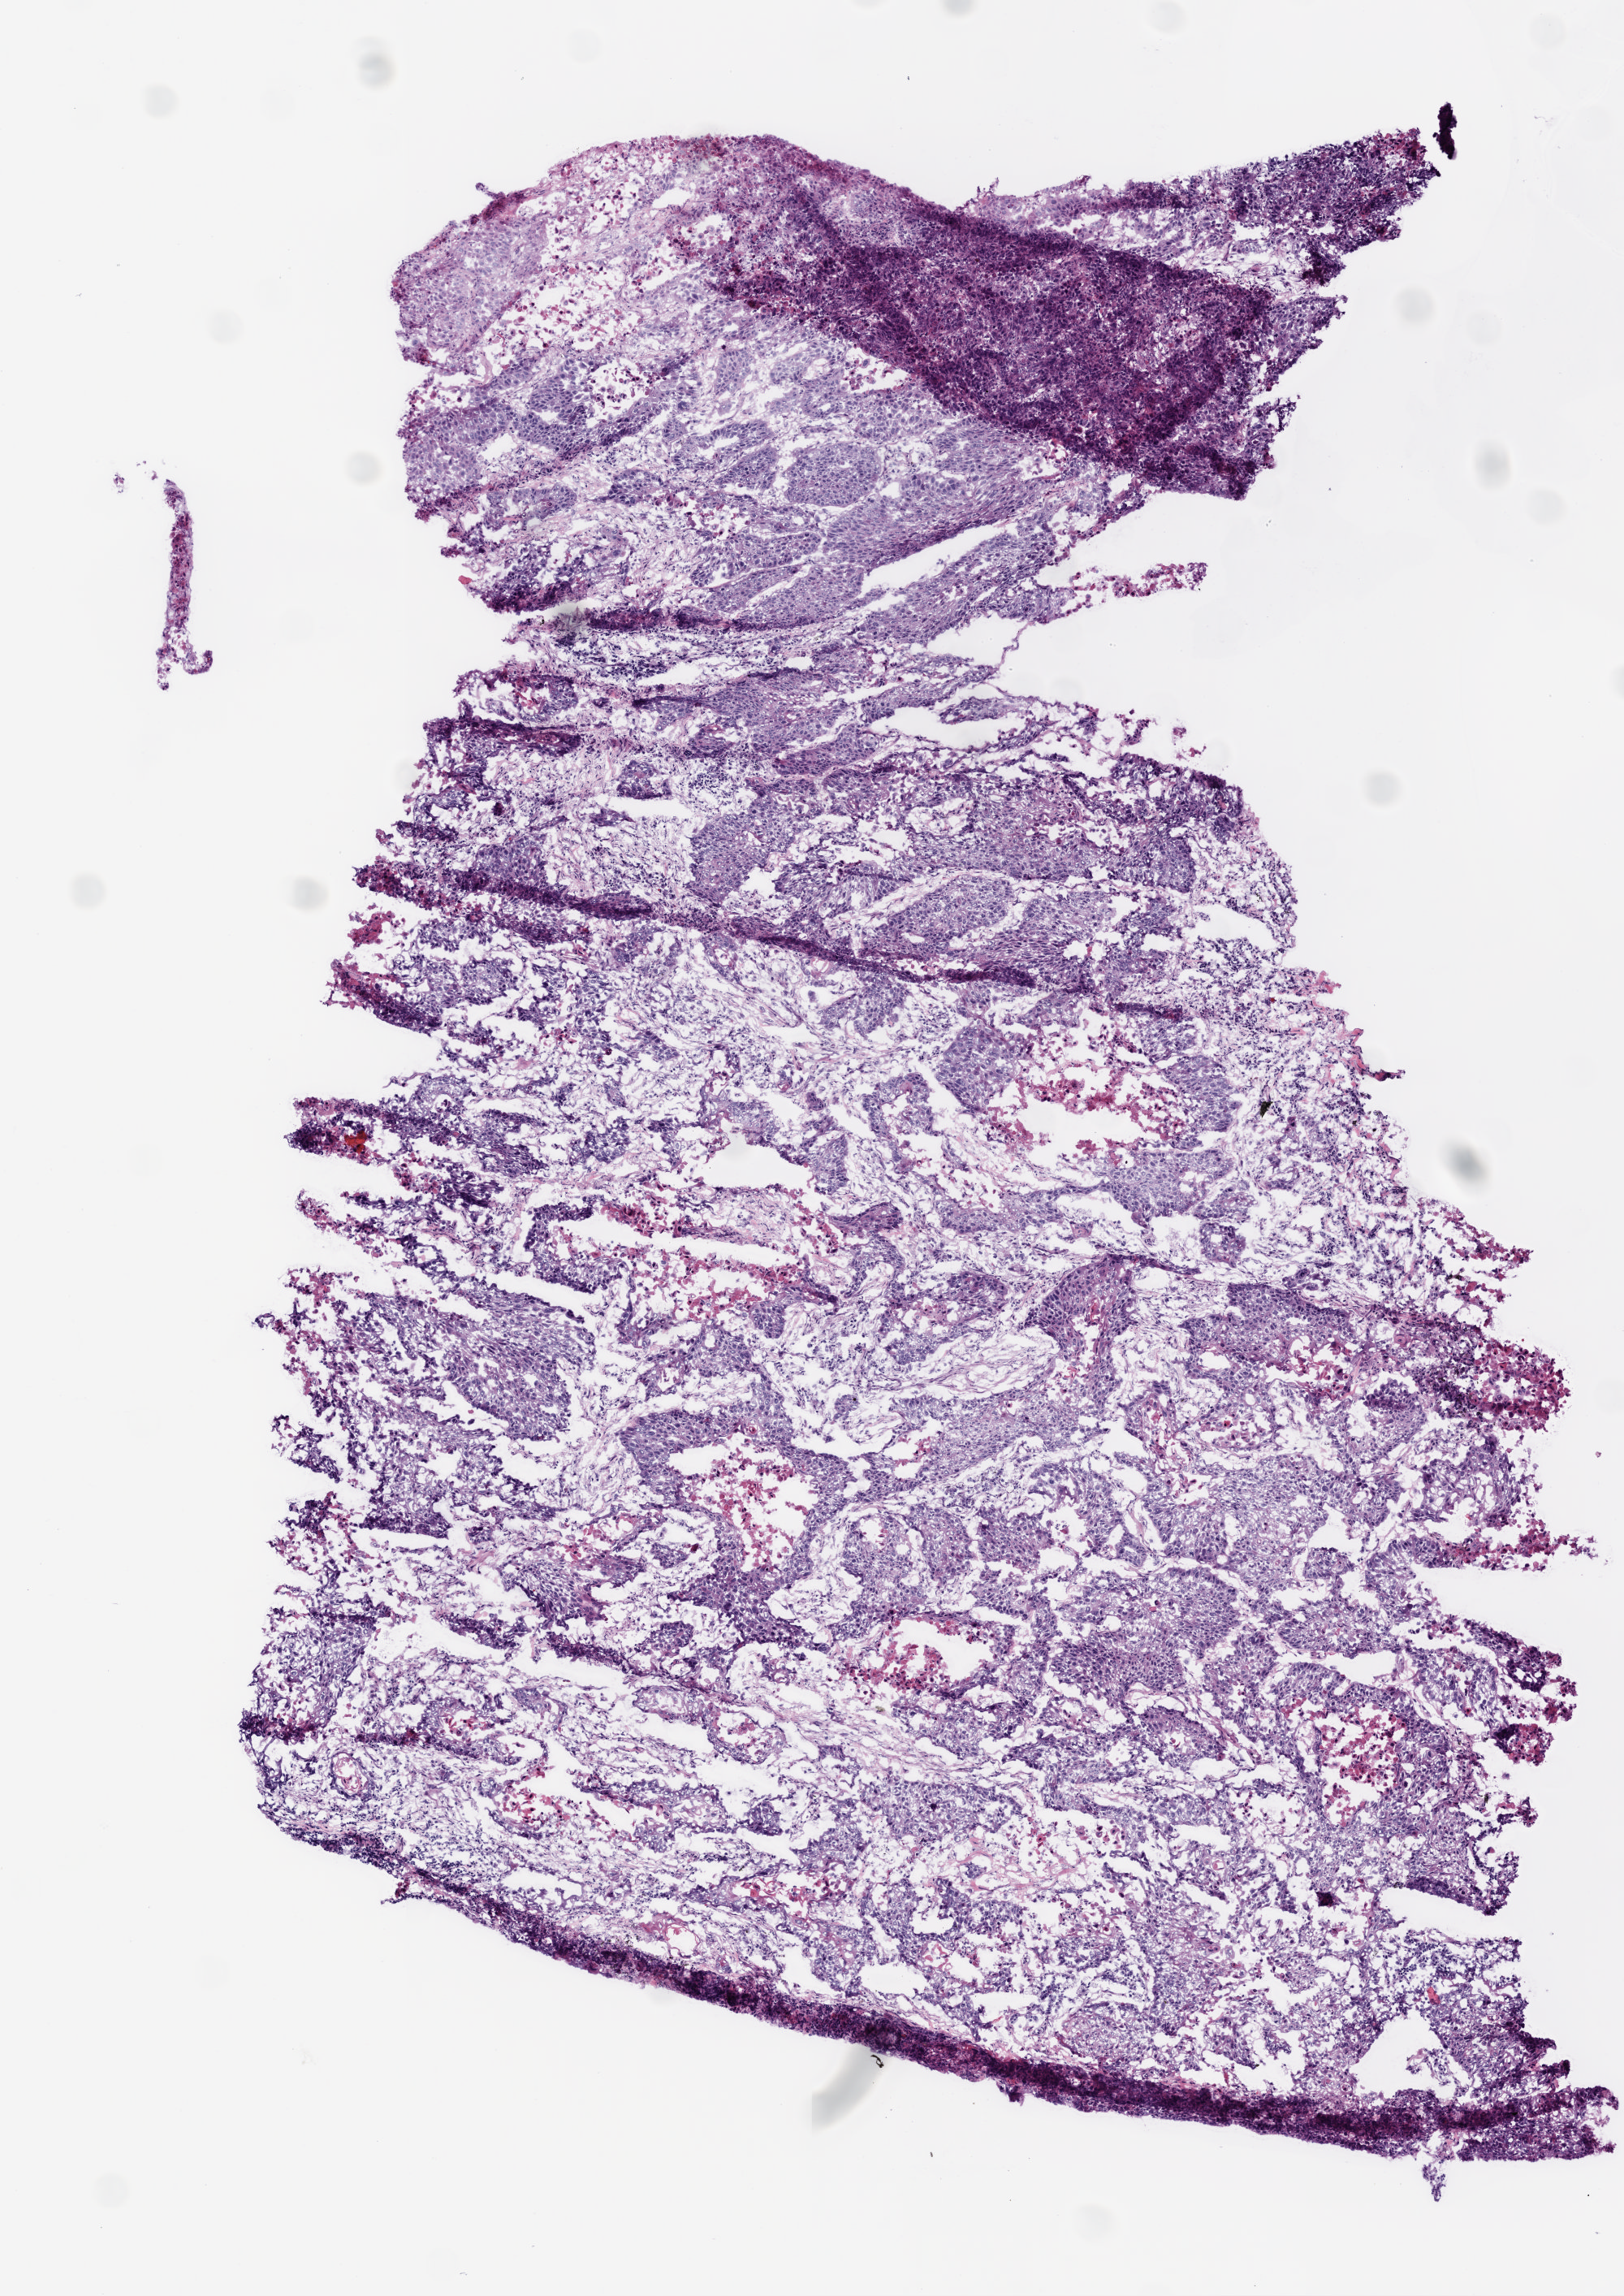
Digitized Hematoxylin and eosin (H&E) stained tissue section (whole slide) — whole scanned area (about 4.0 x 5.7 mm, acquisition: 20x scan) shown as a low-resolution overview; frozen section from the top of the tissue portion; lung, primary tumour sample. Patient: male, age at initial diagnosis 52 years. Slide review estimates, as recorded: tumour cells 70%, tumour nuclei 85%, normal cells 0%, stromal cells 22%, necrosis 8%. Inflammatory infiltration, as recorded: lymphocyte infiltration 2%.
AJCC pathologic stage: IB. Pathologic diagnosis: Squamous cell carcinoma, NOS (lower lobe, lung).